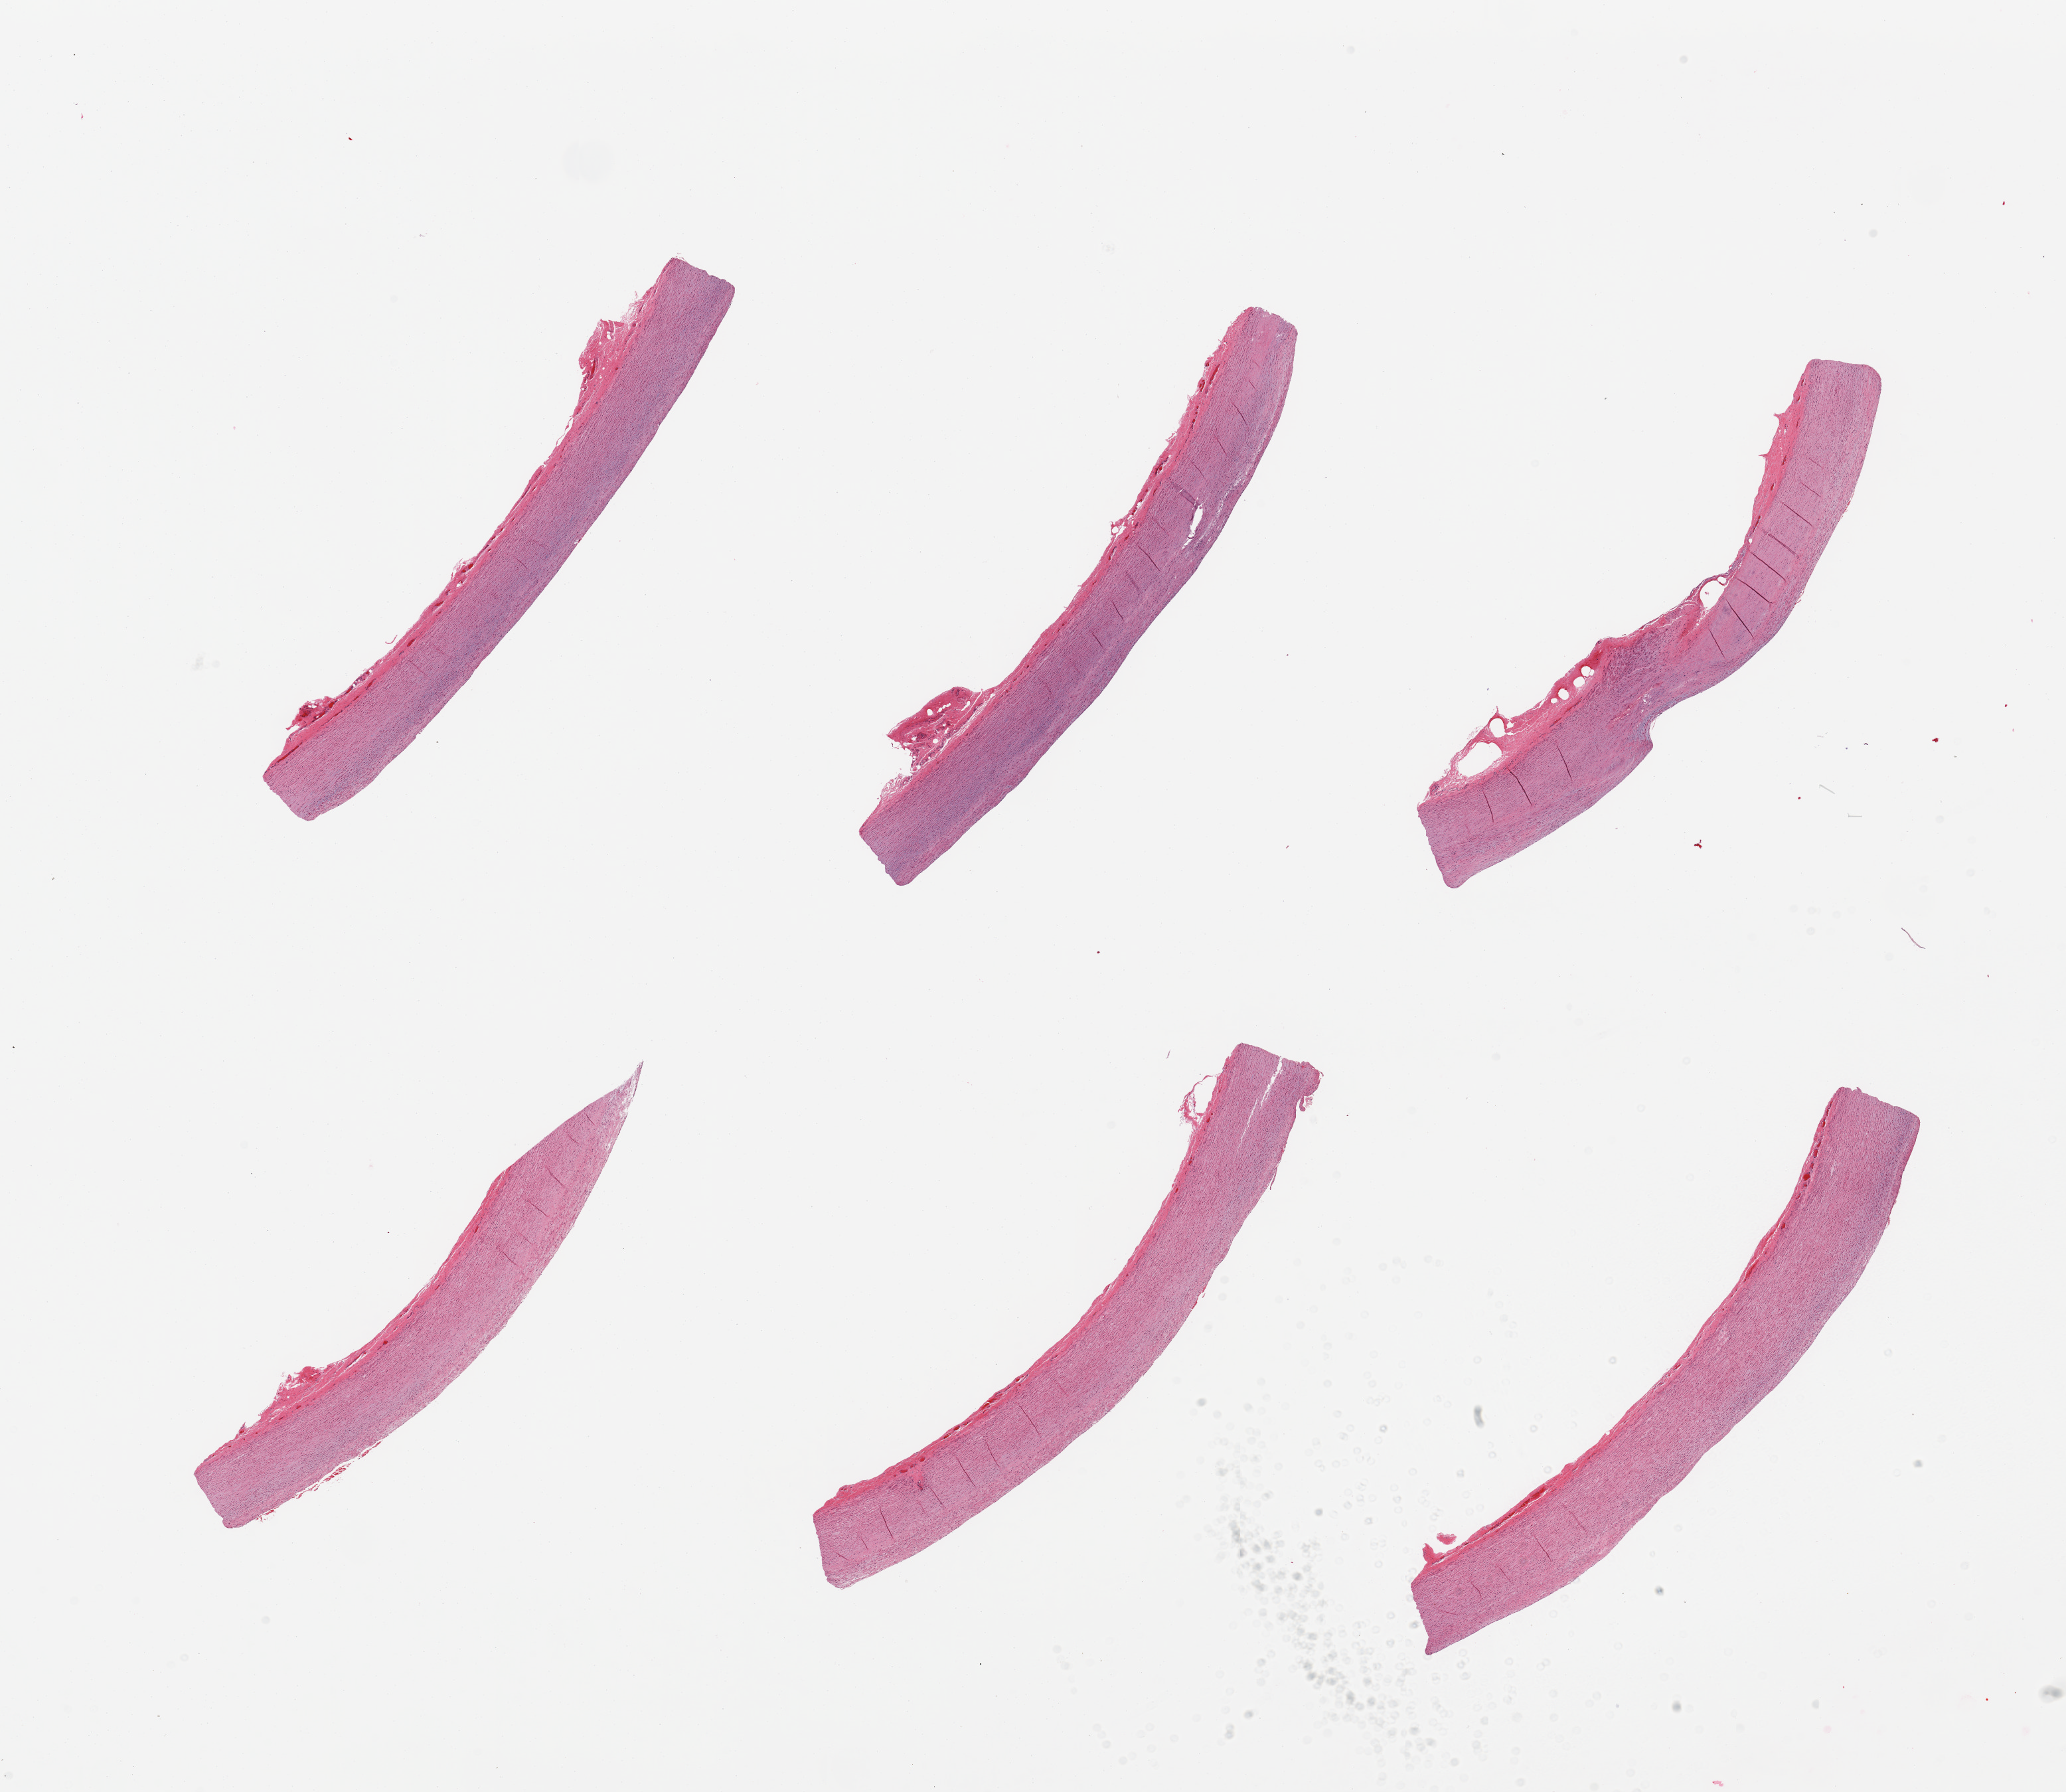
Whole-slide image, H&E stain — whole scanned area (about 24.6 x 21.3 mm, from a 20x scan) shown as a low-resolution overview. PAXgene-fixed, paraffin-embedded tissue. Target tissue: aorta. Donor tissue sample. Donor: male.
• review note (as recorded): 6 pieces; no plaques